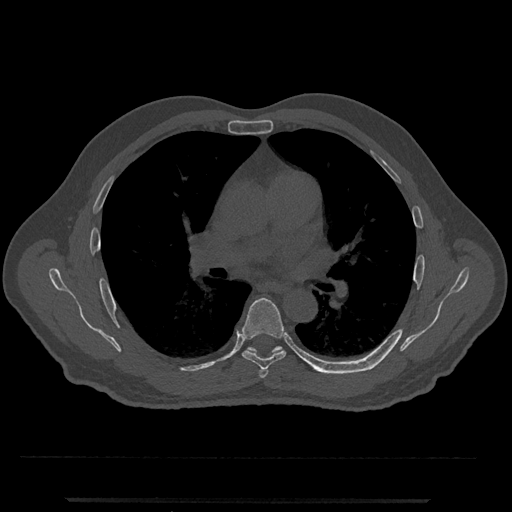
CT including the spine, one axial slice. Slice 728 of 797 in the series (ordered by position). Reconstruction kernel Br40s/3. 120 kVp. Bone window (W 1800 / L 400 HU). 512 × 512 image matrix. Male patient, age 63 years. Case-level facts recorded for this patient, not image findings: primary cancer: prostate.
Structures marked on this image (semi-automatically segmented with operator editing):
- T5 vertebra: box from (x=259, y=369) to (x=268, y=378) px
- T6 vertebra: (x=241, y=298)–(x=286, y=370)
- T7 vertebra: (x=246, y=346)–(x=326, y=374)